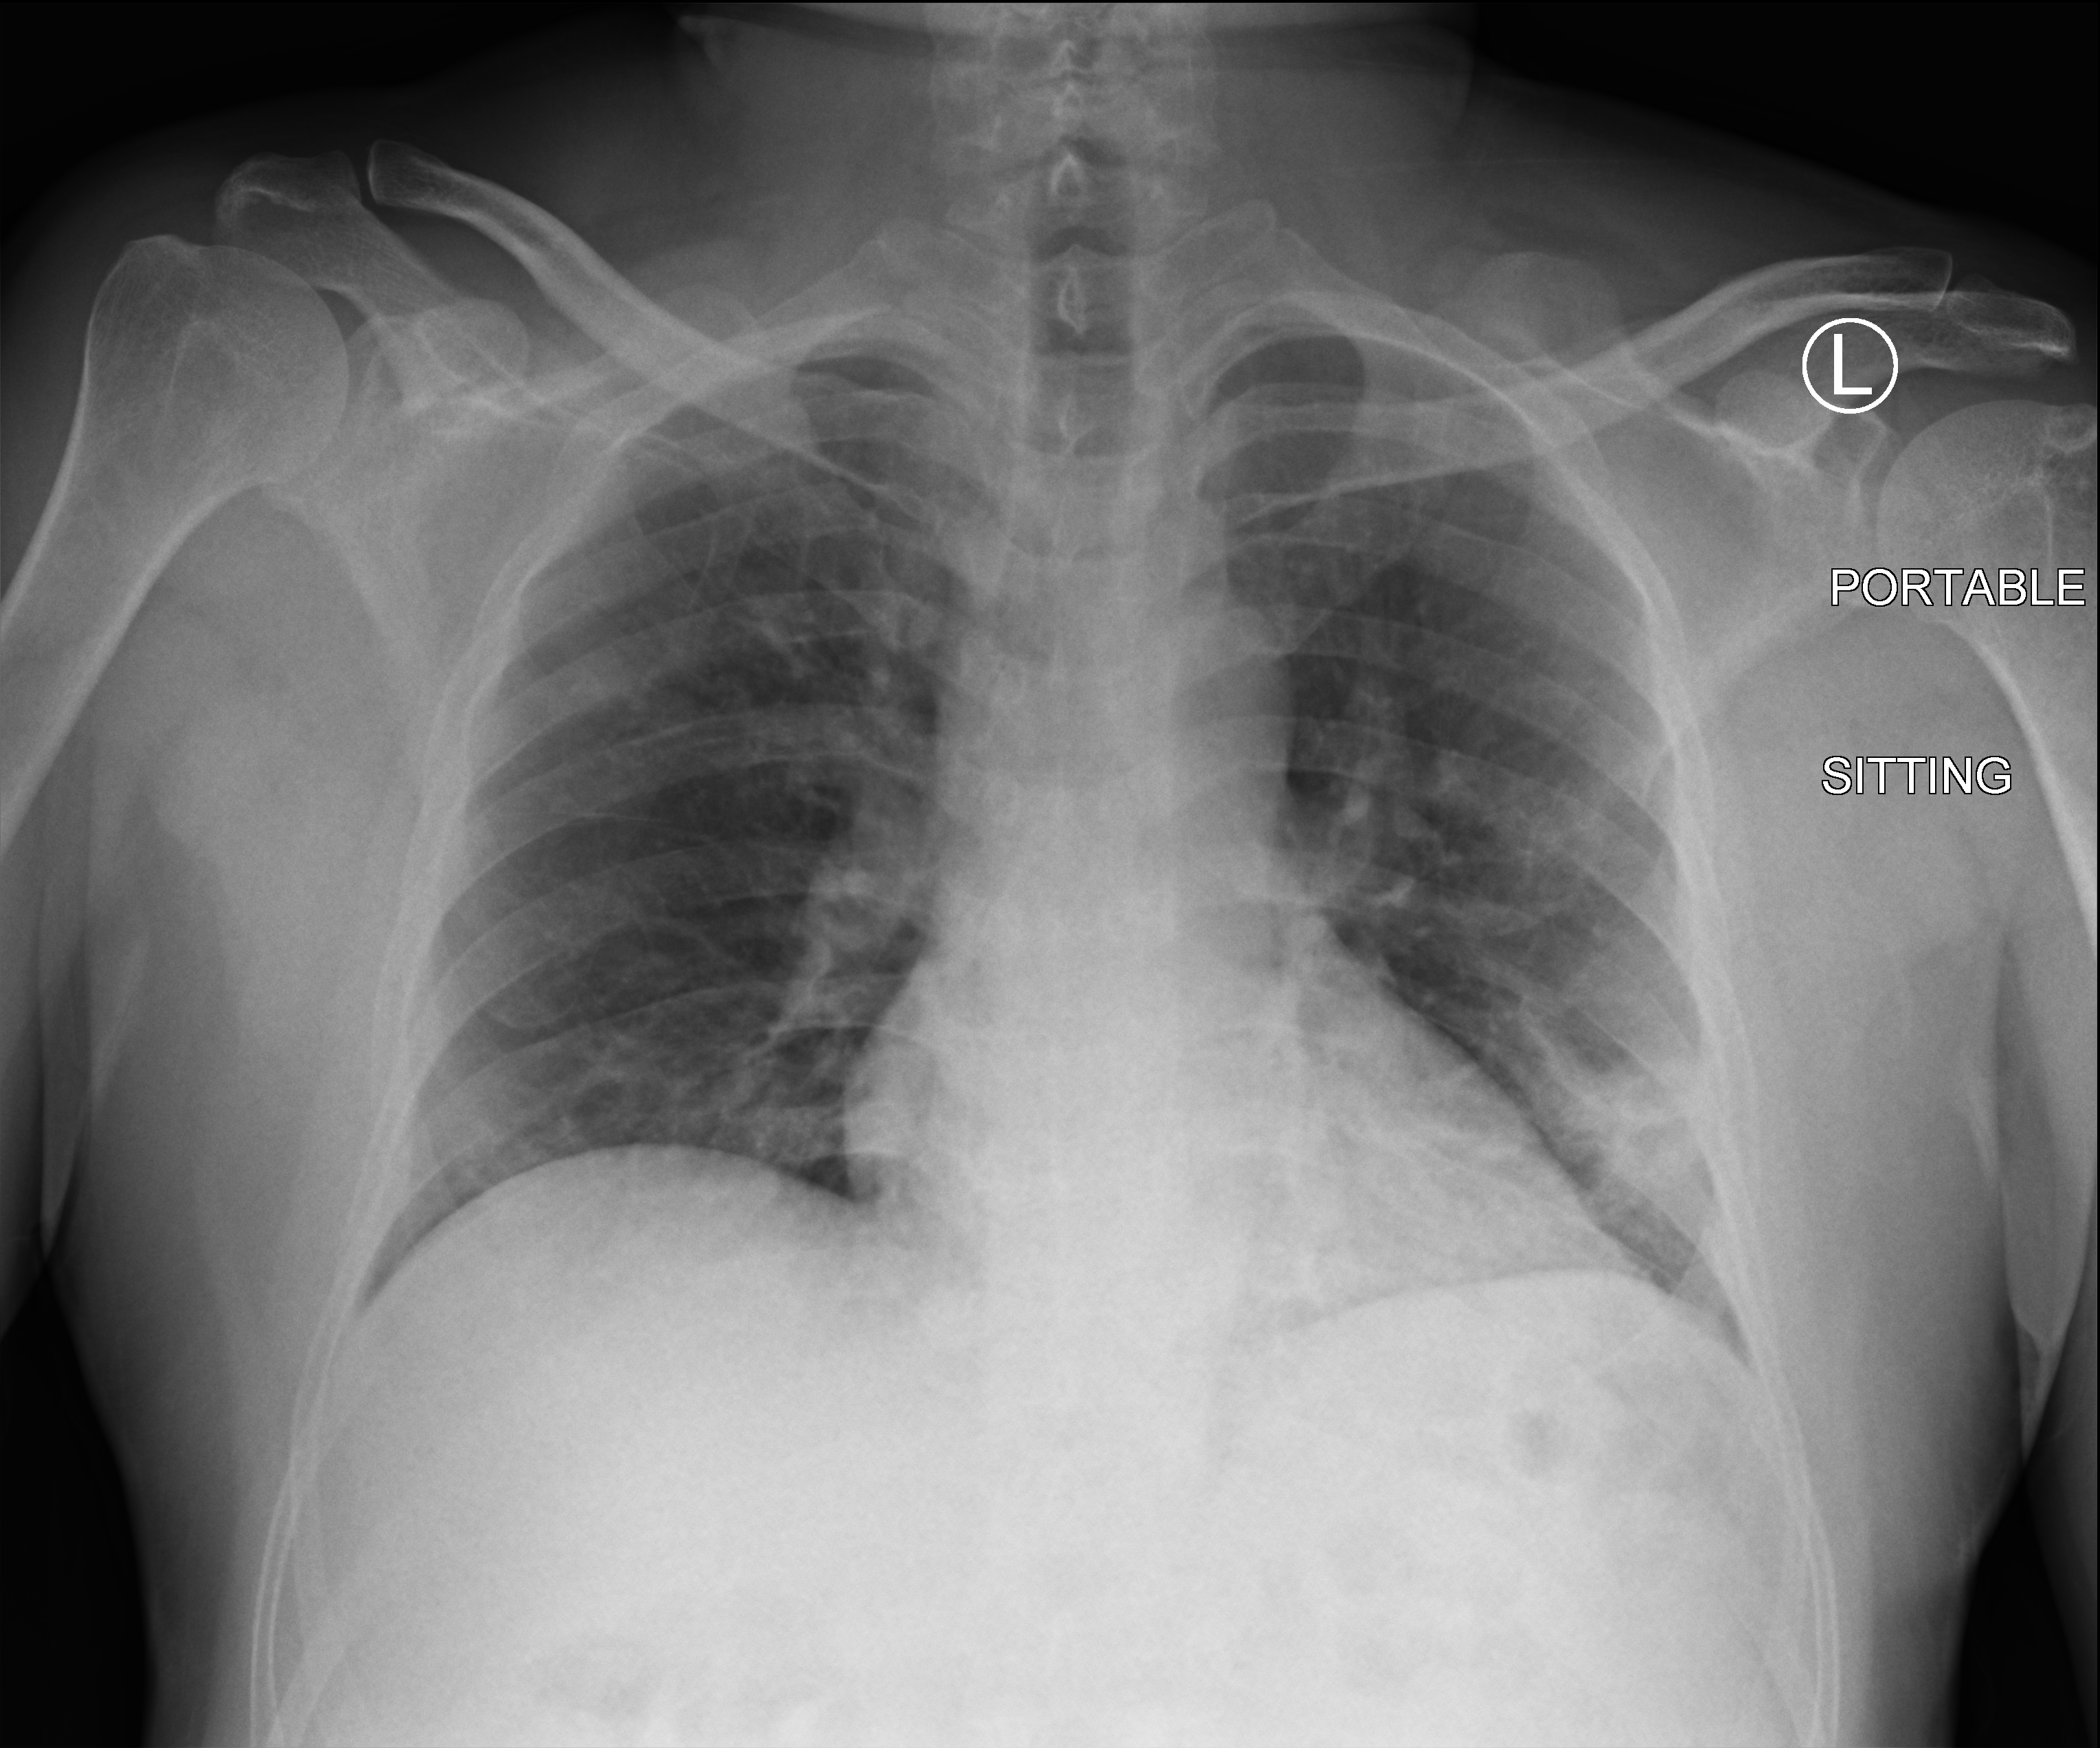
Portable chest radiograph; anteroposterior (AP) projection. Male patient hospitalised with COVID-19, age 18–59 years.
Hospital-stay facts (about this admission, not read from this image; timing relative to this image not recorded):
- mechanically ventilated during this hospital stay: no